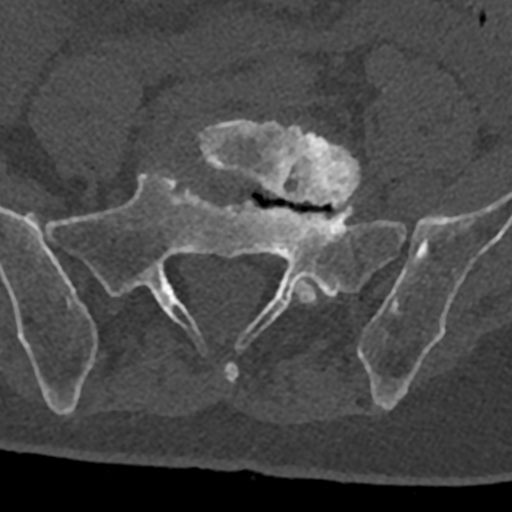
CT including the spine, one axial slice. Reconstruction kernel Br40s/3. 120 kVp. Bone window (W 1800 / L 400 HU). 0.5 mm slice thickness. 512 × 512 image matrix. Male patient, age 74 years. Case-level facts recorded for this patient, not image findings: primary cancer: renal.
Annotated regions visible in this slice (semi-automatic segmentation, software-assisted and operator-edited):
- L5 vertebra: bounding box <196,120,360,304> (left, top, right, bottom; pixels)